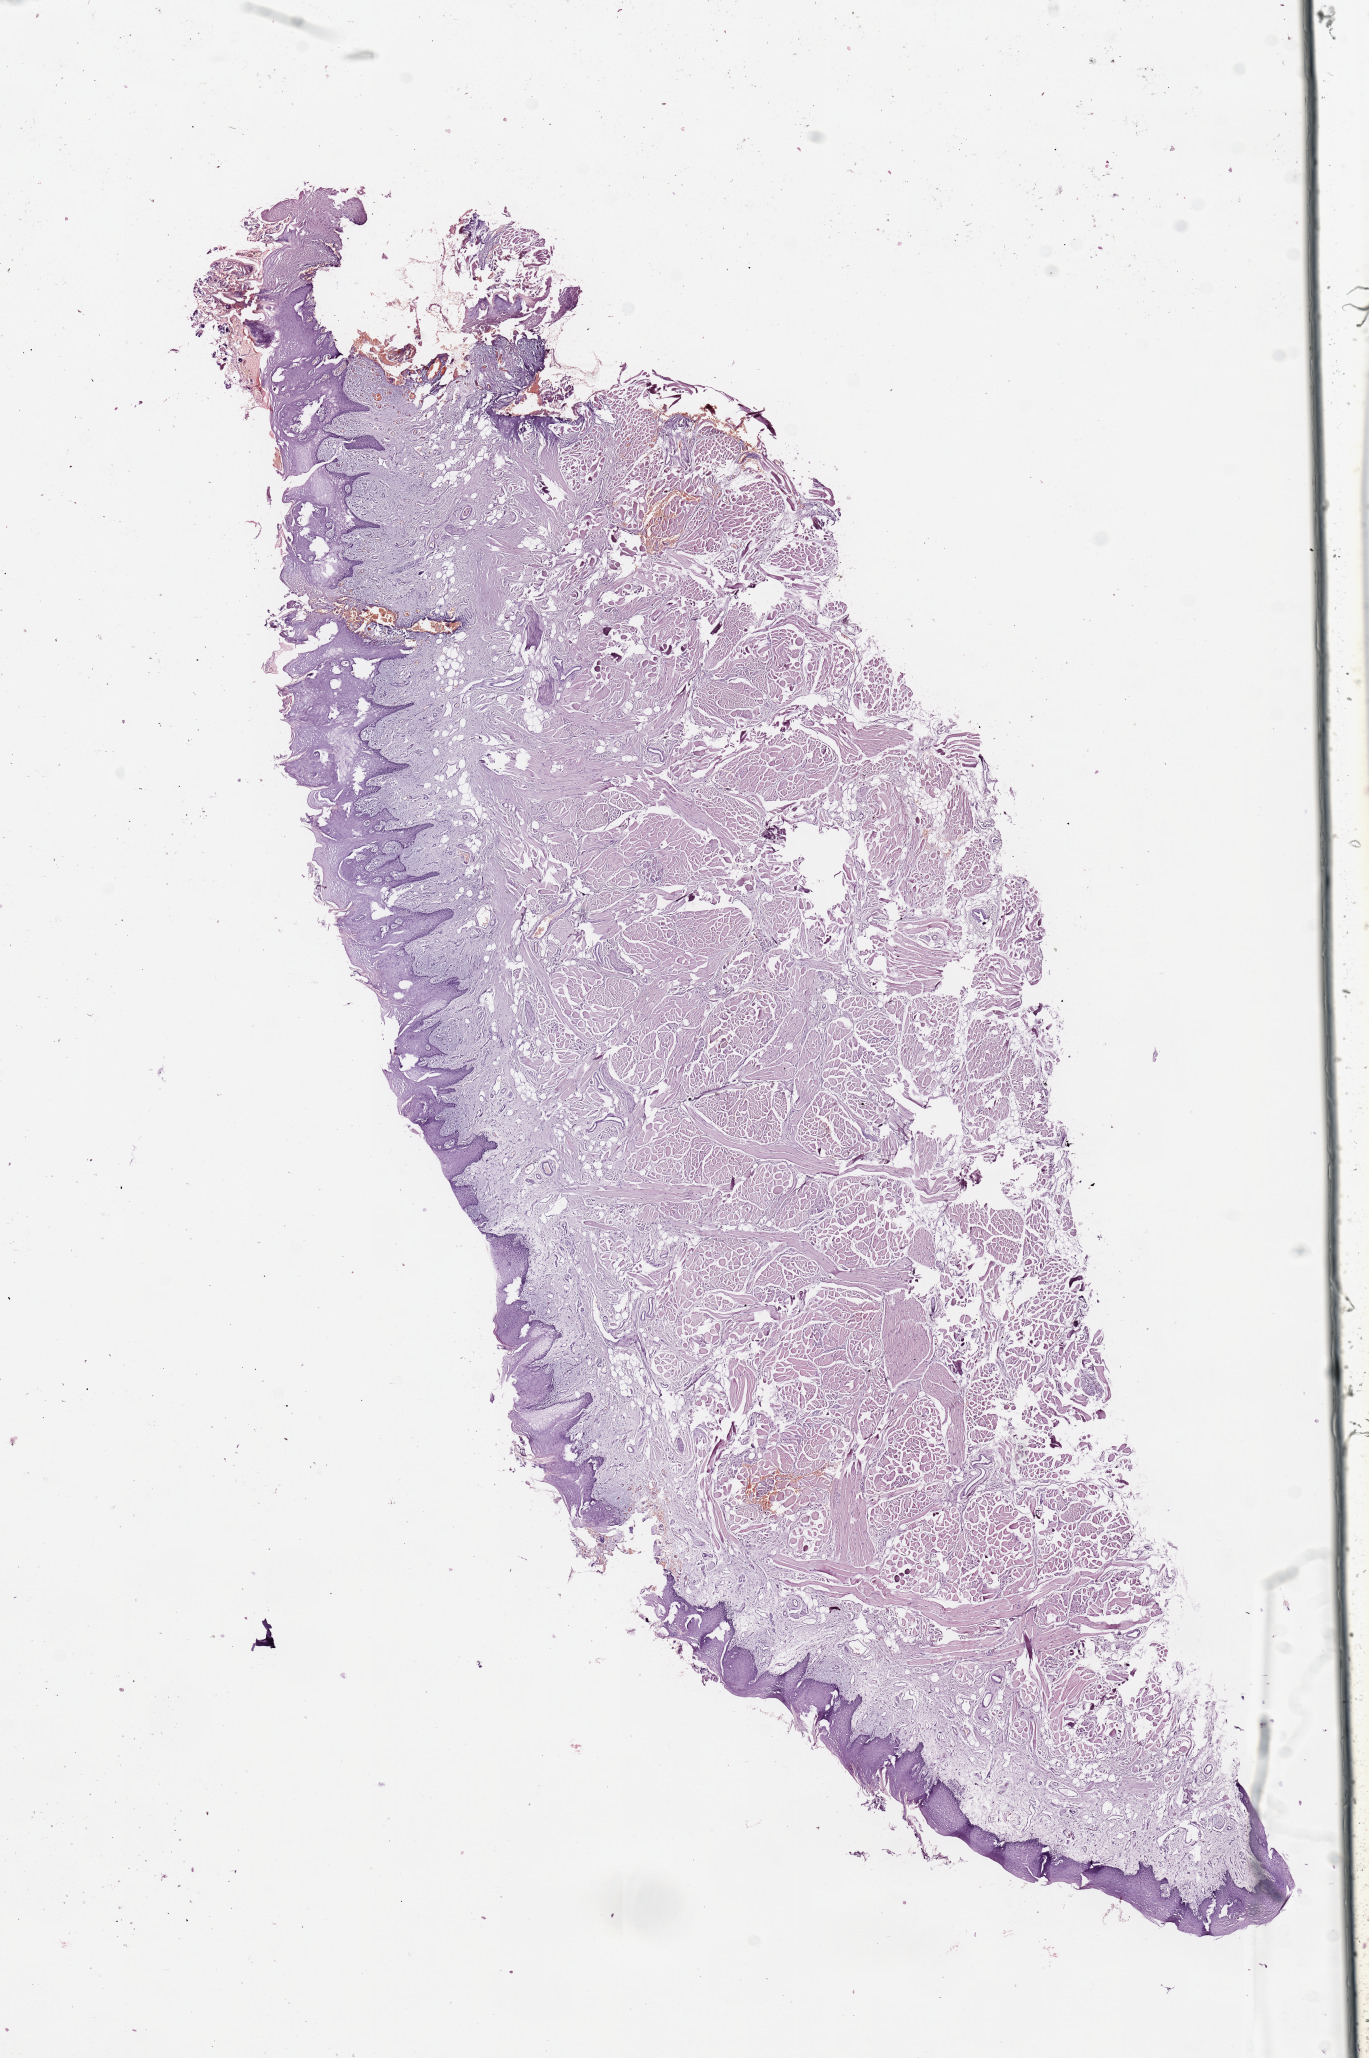
Hematoxylin and eosin (H&E) stained whole-slide image, a low-resolution overview of the entire scanned area, about 10.8 x 16.3 mm; normal (non-tumour) tissue sample, sampled site: tongue. 64-year-old male patient.
• this section: normal (non-tumour) tissue from the same patient
• patient diagnosis: Squamous cell carcinoma, NOS (base of tongue, NOS)